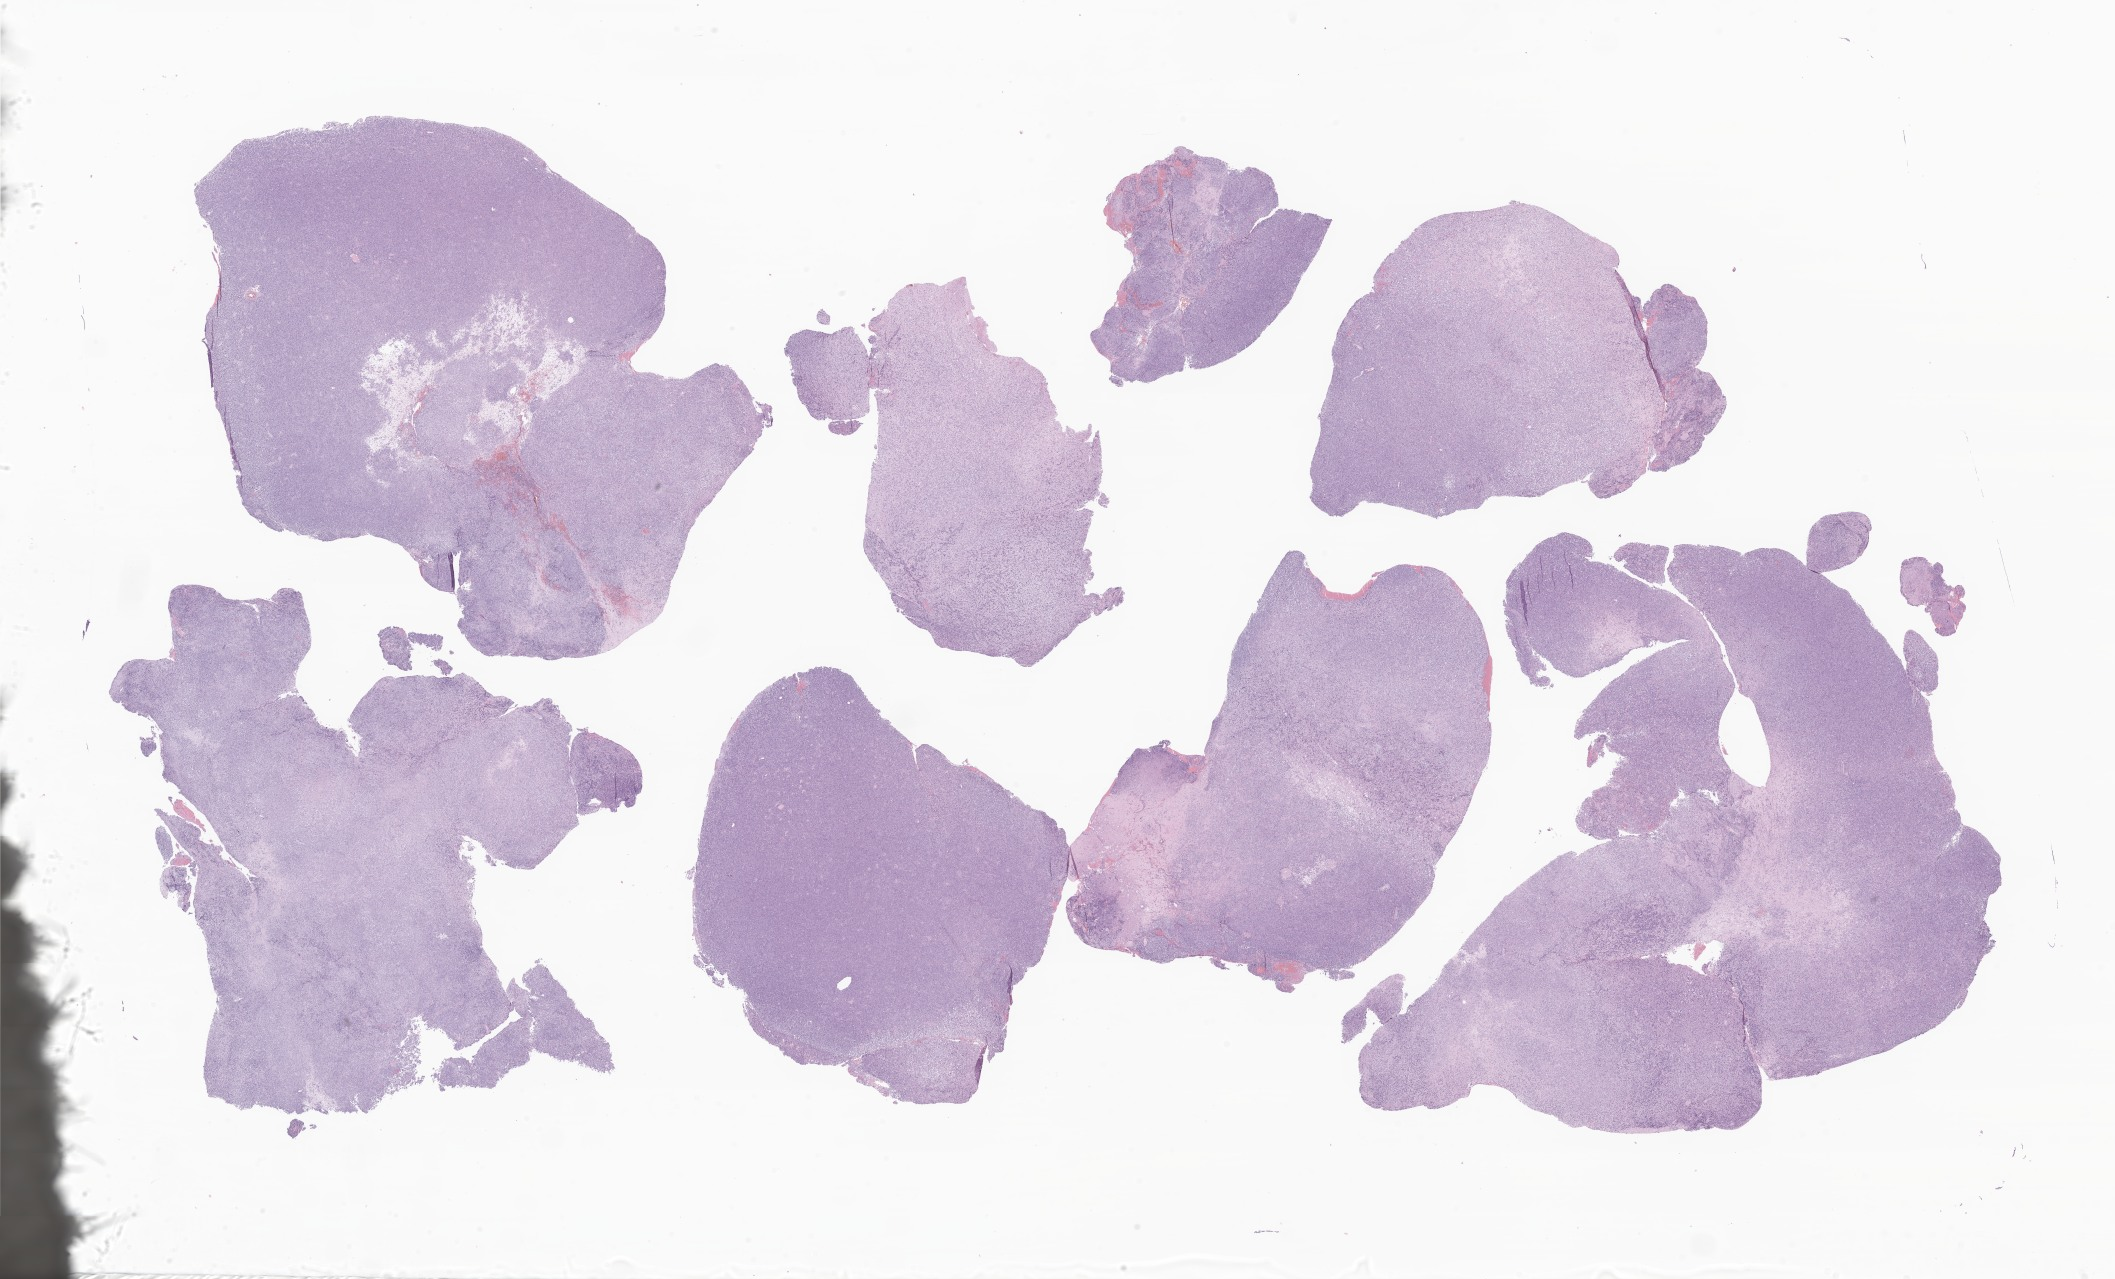
Digitized hematoxylin and eosin (H&E)-stained section of tumor tissue from the temporal lobe — shown as a low-resolution overview of the whole scanned area (about 35.7 x 21.6 mm), formalin-fixed, paraffin-embedded (FFPE) tissue. Male patient, age 85 months (7 years 1 month).
- recorded diagnosis: Neoplasm, uncertain whether benign or malignant